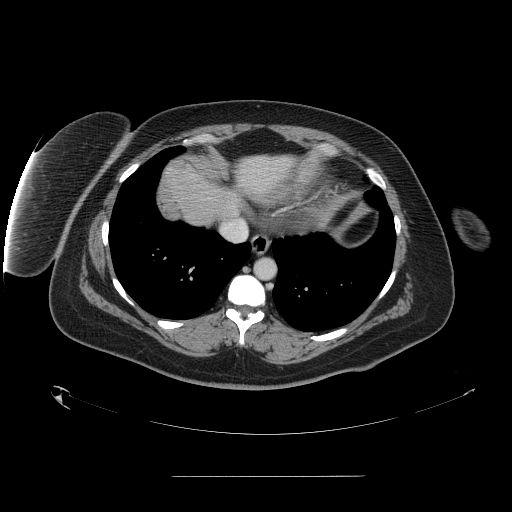
Contrast-enhanced abdominal CT, one axial slice. Position 142 of 164 along the scan axis. 120 kVp. Soft-tissue window (W 400 / L 40 HU). 512 × 512 image matrix, field of view 495 × 495 mm. Female patient, age 52 years. Case-level facts recorded for this patient, not image findings: diagnosis: colorectal cancer liver metastases, imaged before liver resection; multiple liver metastases: yes; largest metastasis: 3.5 cm; chemotherapy before resection: no.
Structures marked on this image (outlined manually by an expert reader):
- liver: bounding box (x1, y1, x2, y2) in pixels: (166, 164, 277, 226)
- planned liver remnant (the part of the liver to remain after resection): (187, 169, 242, 218)